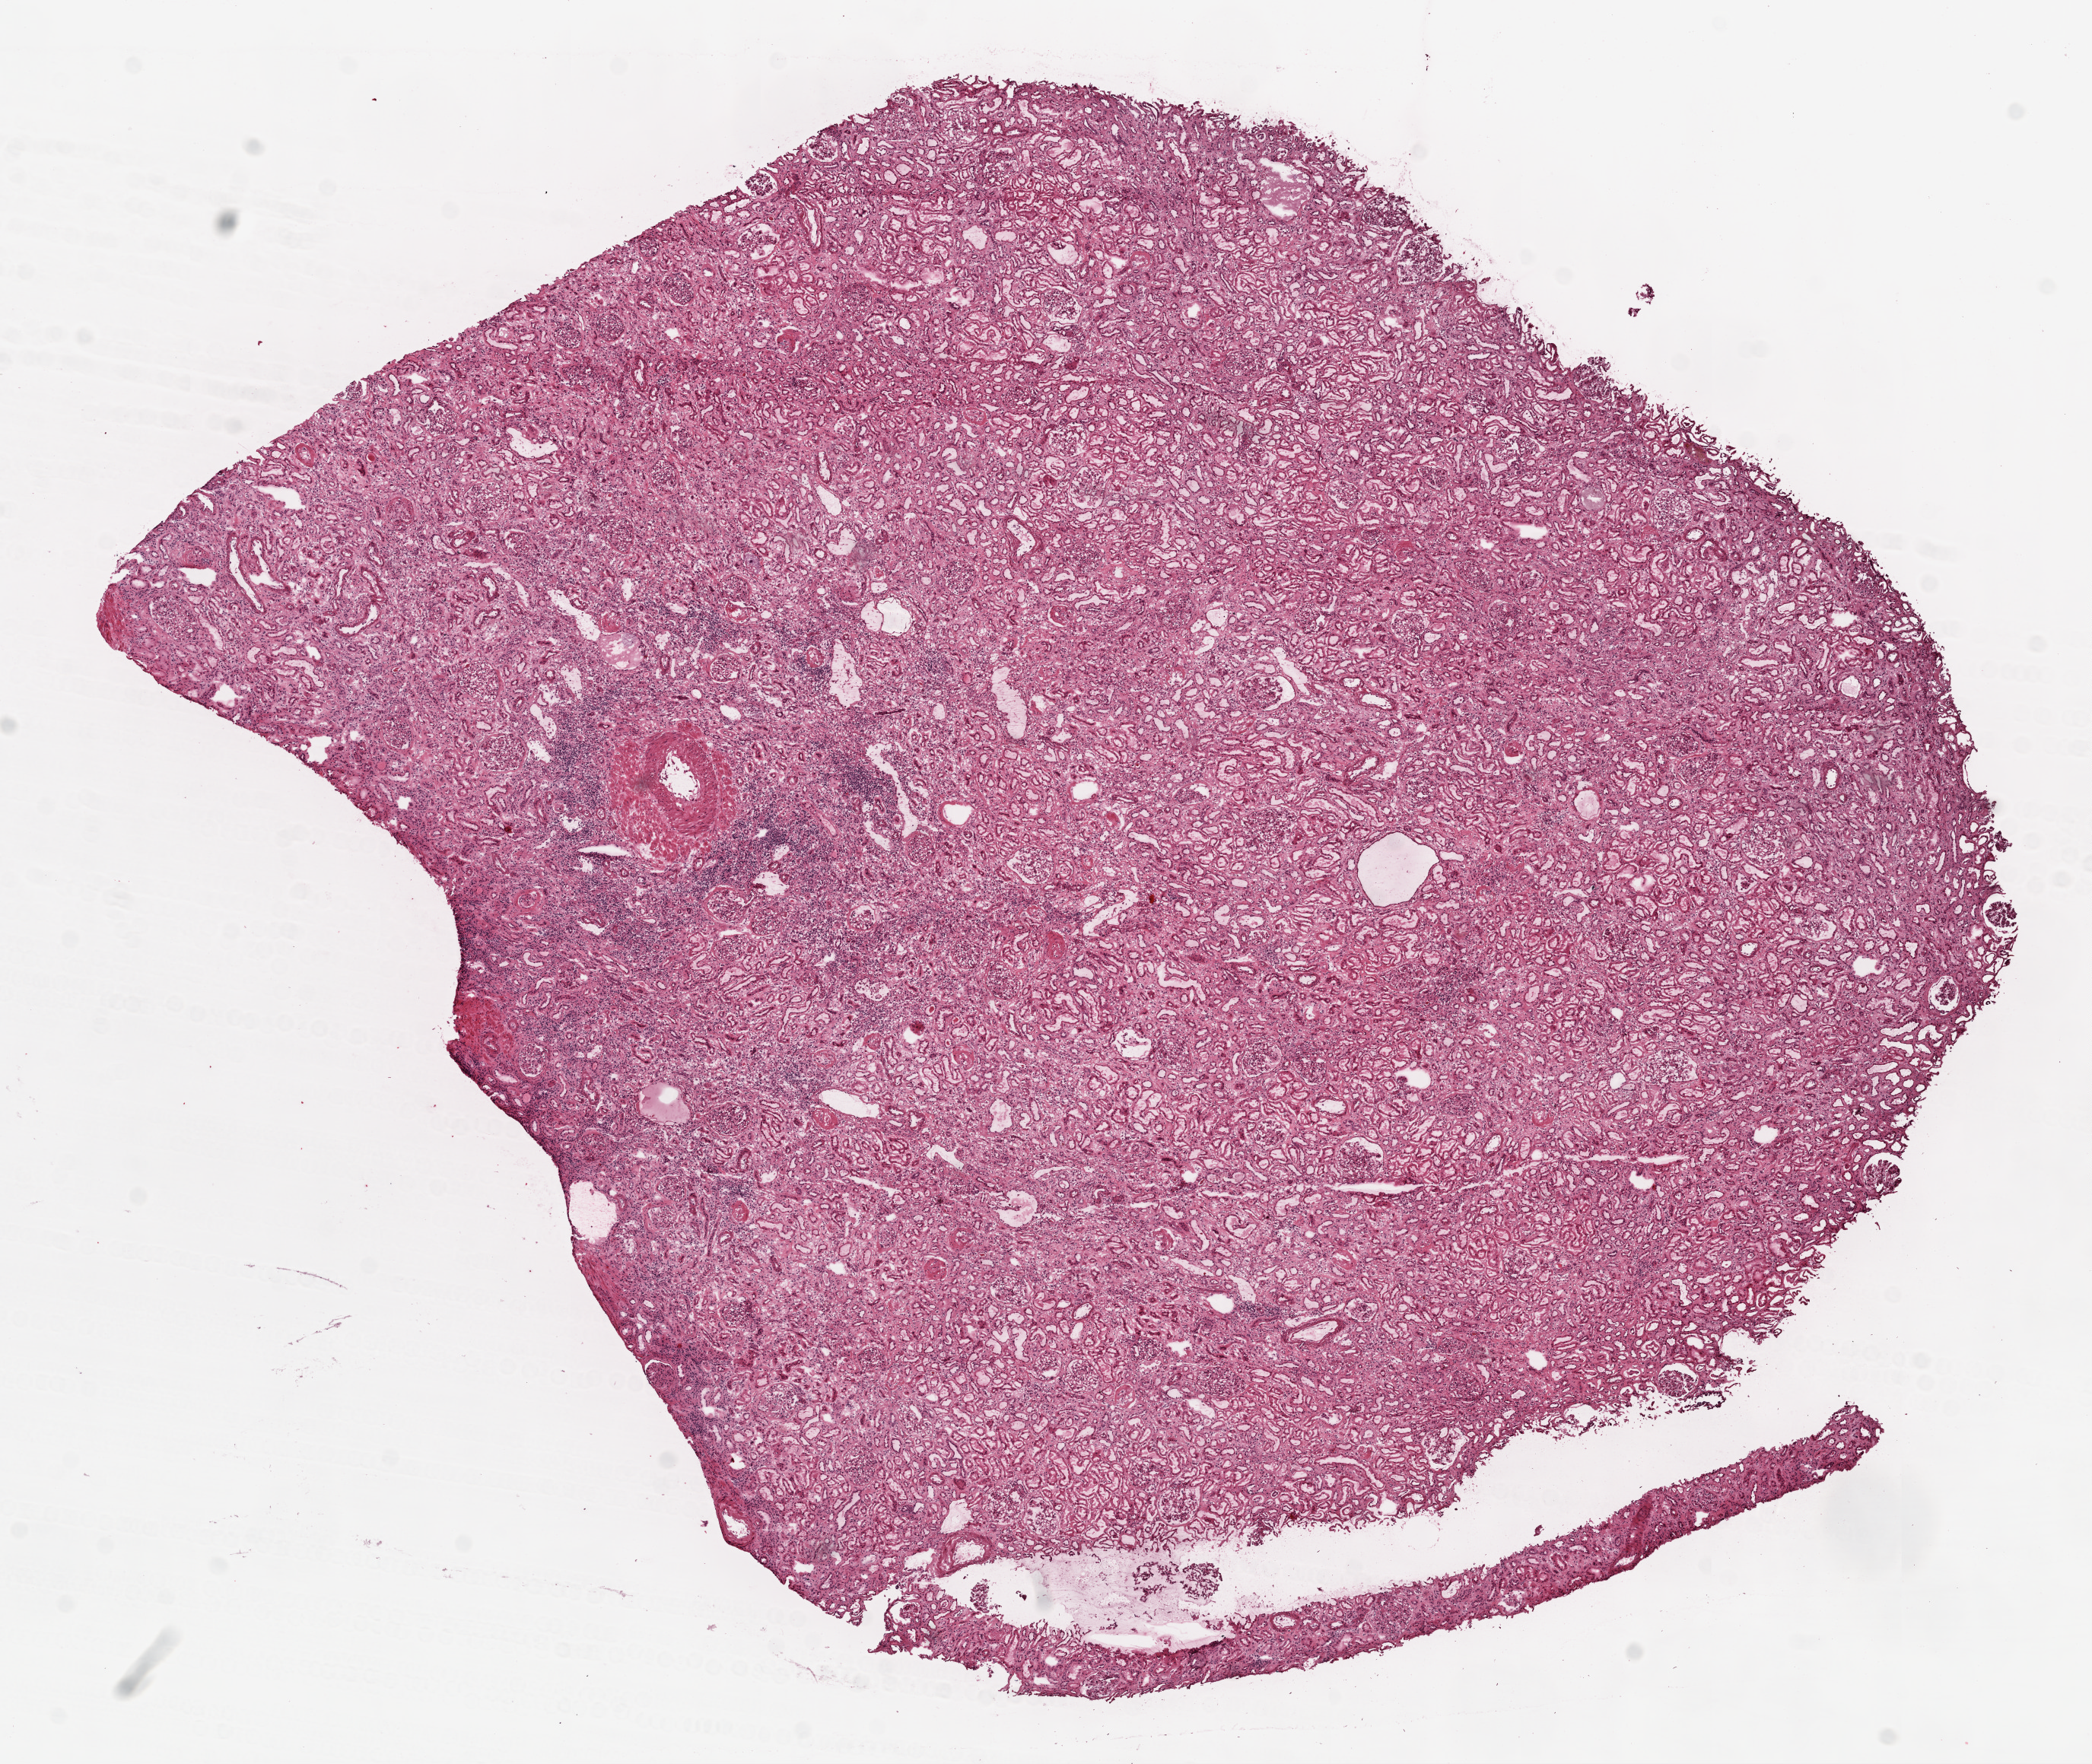
Digitized H&E tissue section (whole slide) — shown as a low-resolution overview of the whole scanned area (about 11.0 x 9.3 mm, slide scanned at 20x); frozen section; sample: solid tissue normal (non-tumour tissue), kidney. Male, age 70 years at initial diagnosis.
This section: solid tissue normal sample (biorepository sample class). Patient diagnosis: Clear cell adenocarcinoma, NOS.